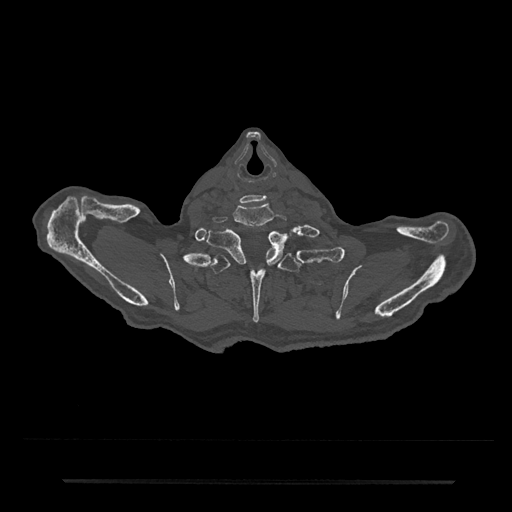
CT including the spine, one axial slice. Position 714 of 797 along the scan axis. Reconstruction kernel Br40s/3. 120 kVp. Bone window (W 1800 / L 400 HU). 0.5 mm slice thickness. 512 × 512 image matrix, field of view 427 × 427 mm. Male patient, age 74 years. Case-level facts recorded for this patient, not image findings: primary cancer: prostate.
Outlined on this slice (semi-automatically segmented with operator editing):
- T1 vertebra: box from (x=207, y=228) to (x=286, y=266) px
- T2 vertebra: (x=202, y=248)–(x=306, y=323)